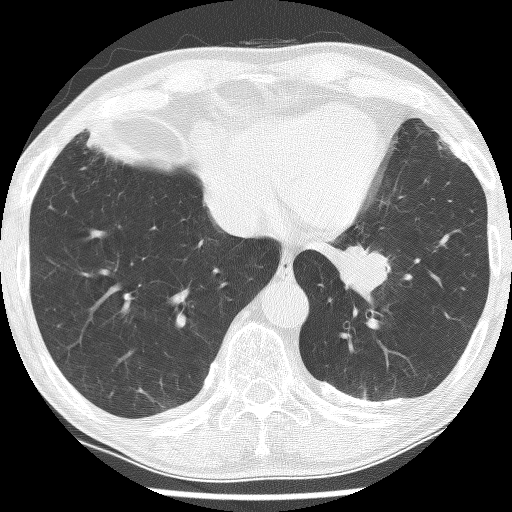
Chest CT (low-dose screening protocol), one axial image. Baseline annual screen. Lung window (W 1500 / L -600 HU). 2.5 mm slice thickness. Lung (sharp) reconstruction kernel (BONE). Male participant, aged 74 years at enrolment. Current smoker at enrolment.
Lesion marked by an expert reader, bounding box [x1, y1, x2, y2] px = [314, 219, 416, 311]. The exam's reader record, not a measurement of the box and not confirmed to be the same lesion: non-calcified nodule or mass ≥4 mm, left lower lobe, 30 × 27 mm, spiculated (stellate) margins, soft tissue attenuation. Official screen result: positive, change unspecified: nodule(s) >= 4 mm or enlarging nodule(s), mass(es), or other non-specific abnormalities suspicious for lung cancer. Participant outcome: lung cancer diagnosed 151 days after this screen — adenocarcinoma, NOS, left lower lobe, stage IIIA (AJCC 6th edition), 49 mm at pathology.